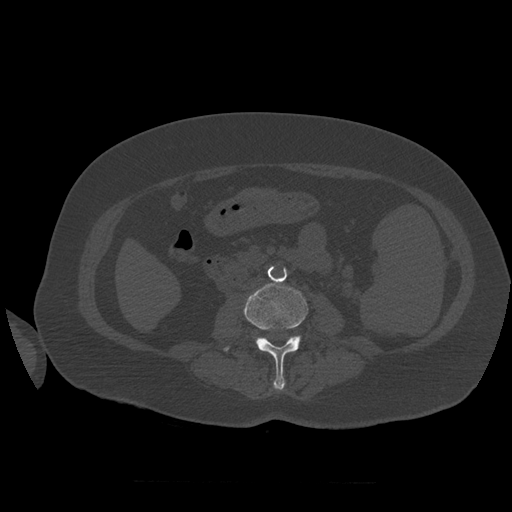
CT including the spine, one axial slice. Position 226 of 399 along the scan axis. Reconstruction kernel STANDARD. 120 kVp. Bone window (W 1800 / L 400 HU). 512 × 512 image matrix, field of view 404 × 404 mm. Patient age 81 years. From the clinical record (not read from this slice): primary cancer: renal; vertebrae with lytic lesions (as recorded): L1.
Outlined on this slice (semi-automatically segmented with operator editing):
- L3 vertebra: bounding box <224,284,308,390> (left, top, right, bottom; pixels)